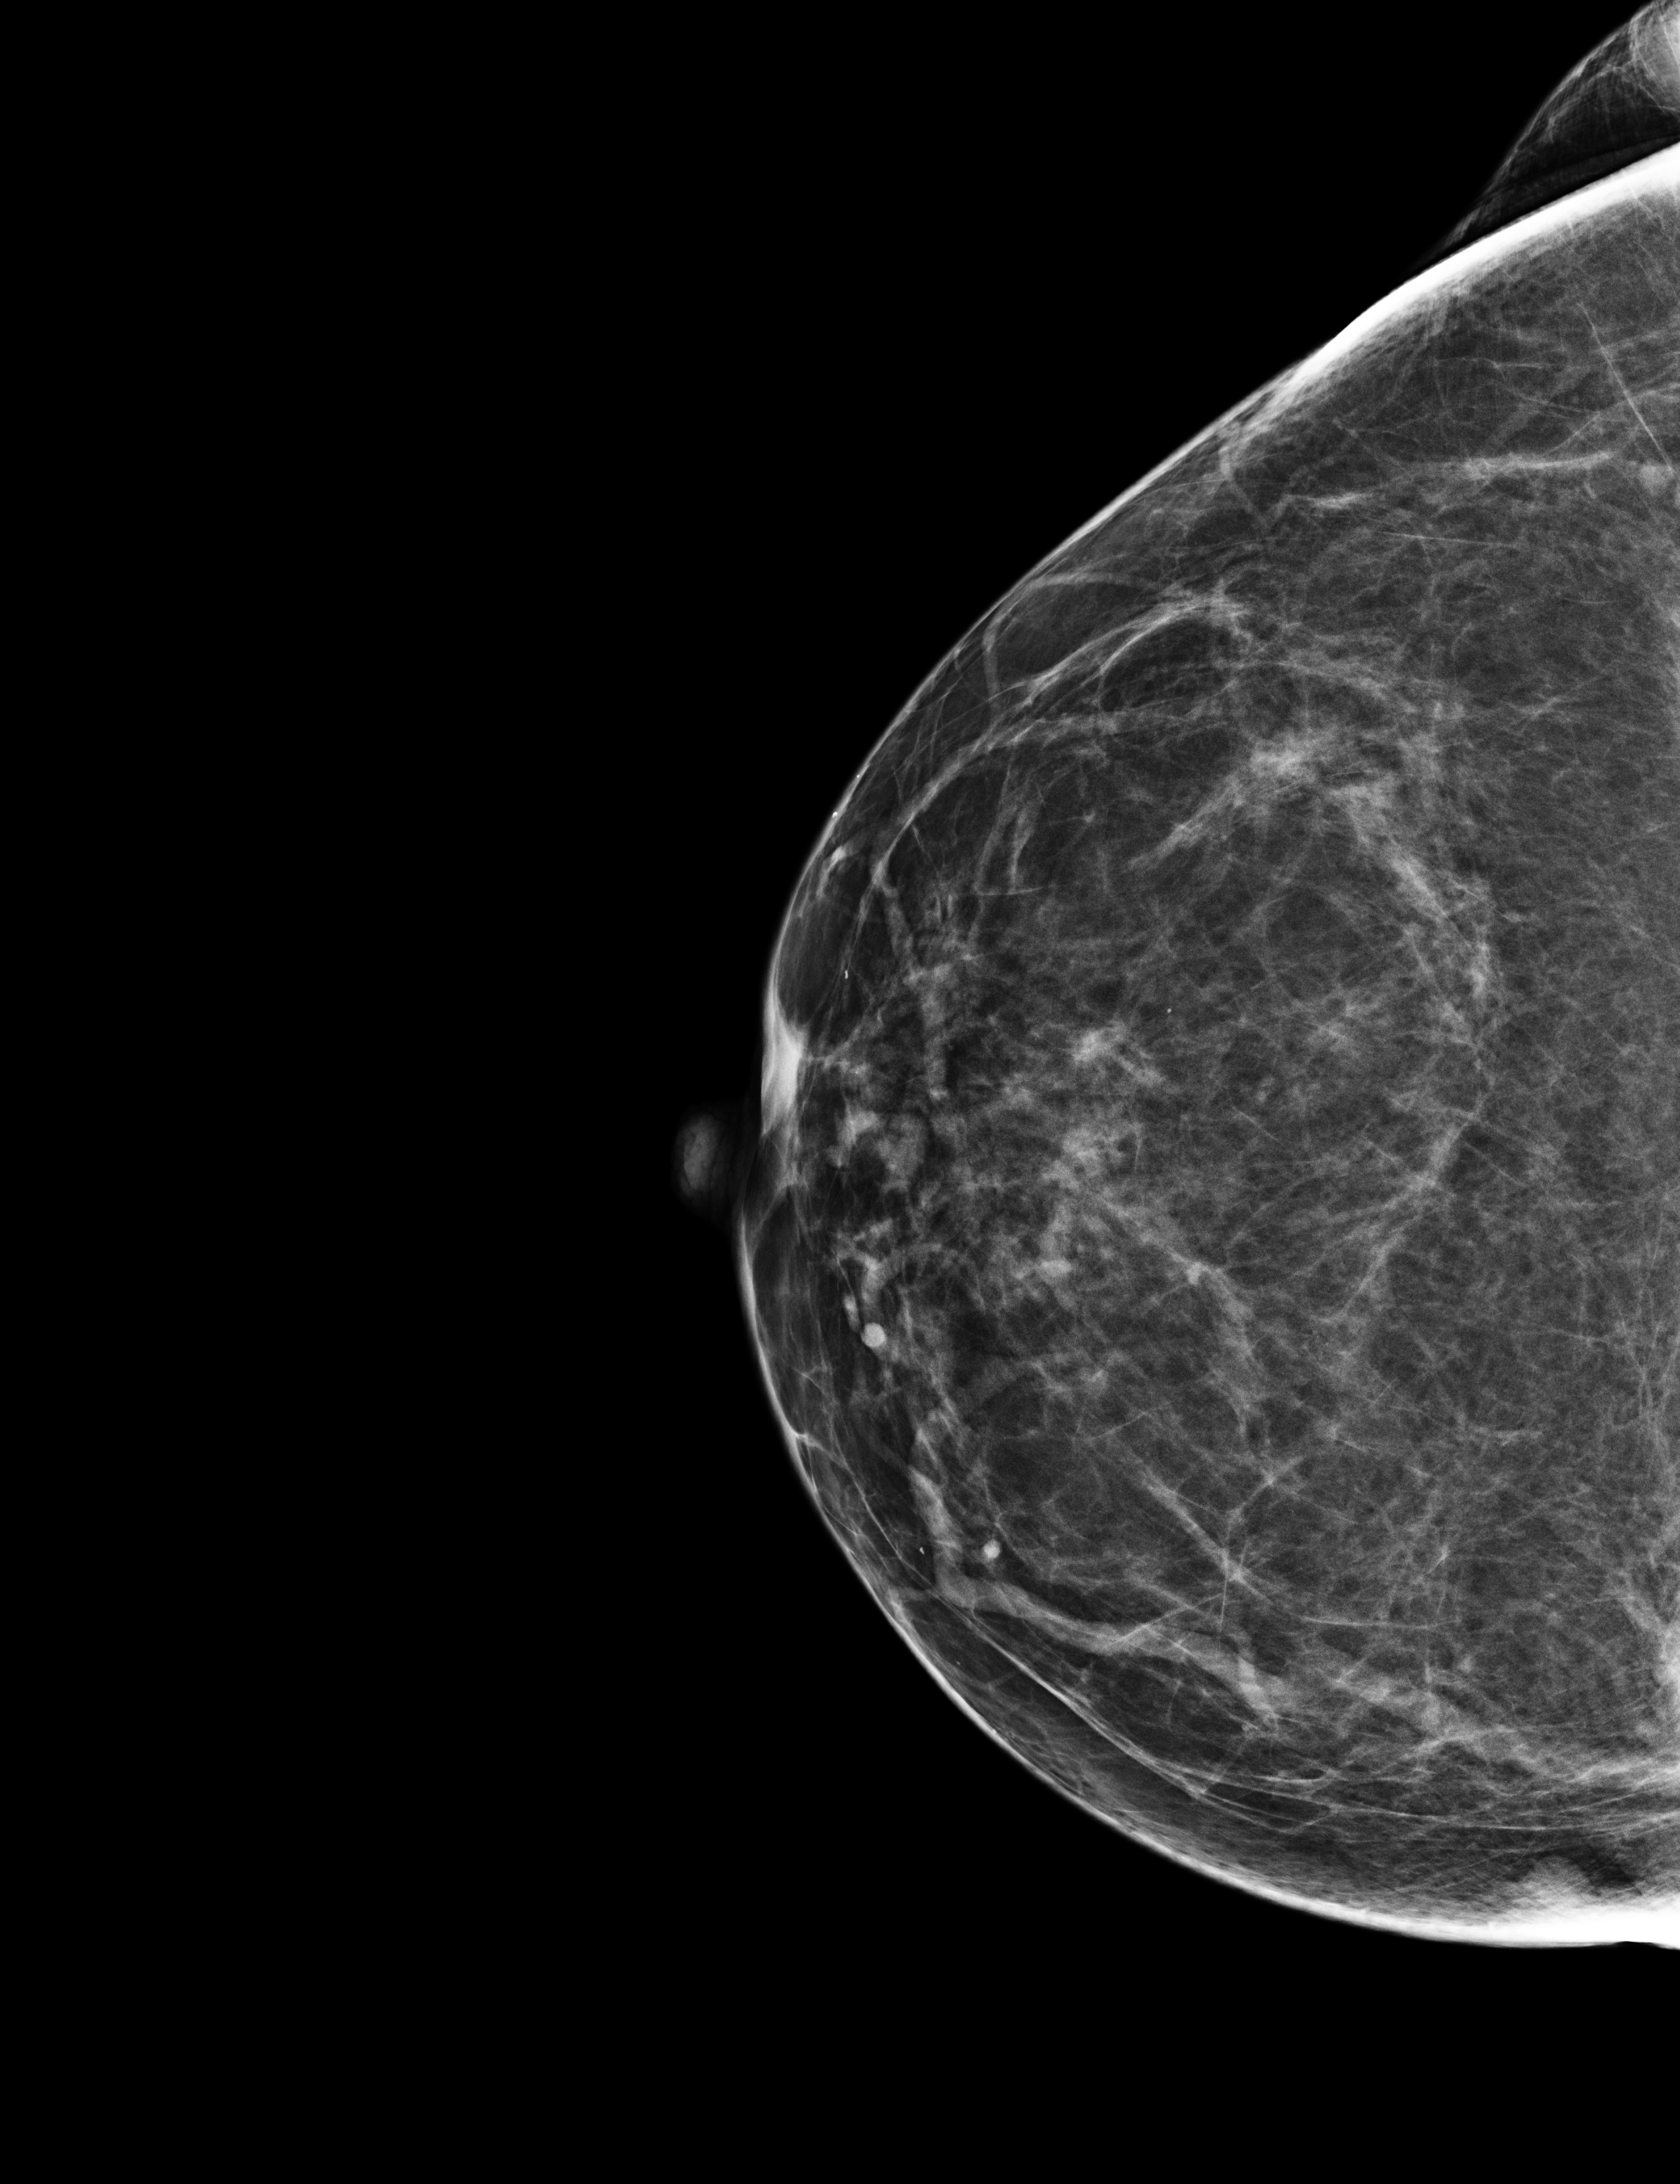
Screening examination, compressed breast thickness 73 mm, system: Selenia Dimensions. Patient aged 55 years (female).
Image type: full-field digital mammogram. Breast: right. Projection: cranio-caudal projection.